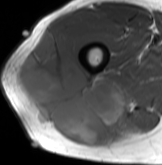
MRI of an extremity soft-tissue mass, one axial slice. Position 53 of 61 along the scan axis. MR volume resampled by the dataset authors to the PET/CT grid (not the native acquisition matrix). 3.27 mm slice thickness. 162 × 165 image matrix. Male patient. Case-level facts recorded for this patient, not image findings: histological type: poorly differentiated synovial sarcoma; grade: high; site of the primary tumour: right buttock.
Structures marked on this image (expert contour drawn on MRI and transferred to this co-registered scan by the dataset authors):
- gross tumour volume including surrounding oedema: bounding box <14,31,124,146> (left, top, right, bottom; pixels)
- gross tumour volume (mass): <14,31,122,146>